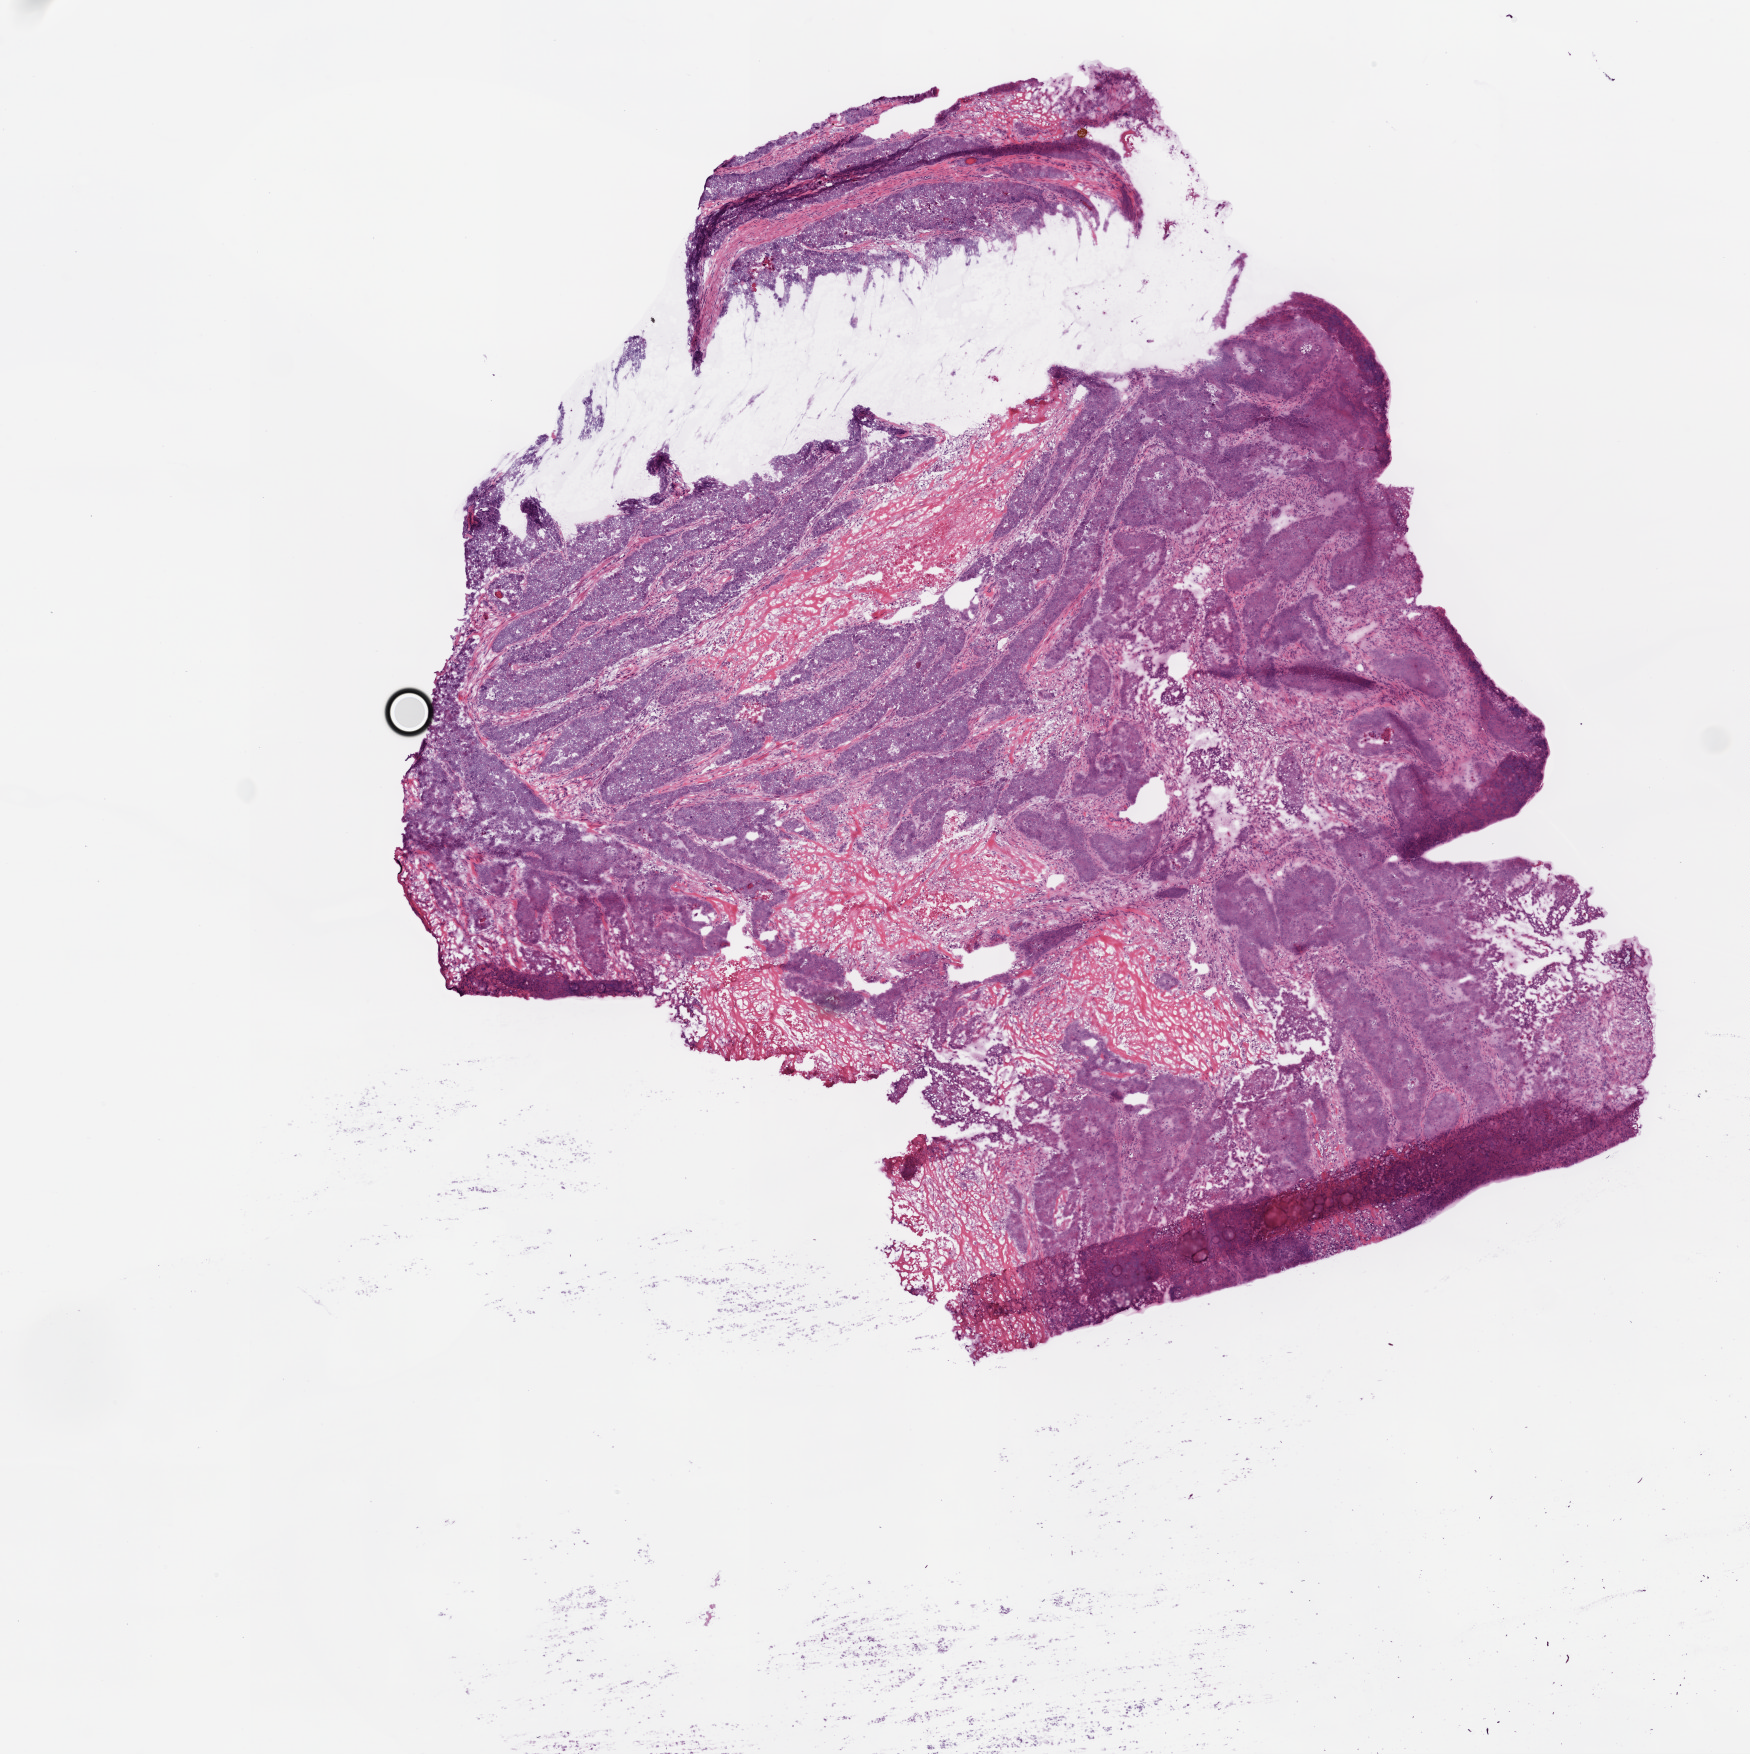
Digitized H&E-stained tissue section (whole slide), whole scanned area (about 7.0 x 7.0 mm, slide scanned at 20x) shown as a low-resolution overview. Frozen section from the top of the tissue portion. Sample: primary tumour, colon. Patient: male, age at initial diagnosis 68 years. Slide review estimates, as recorded: tumour cells 65%, tumour nuclei 90%, normal cells 0%, stromal cells 34%, necrosis 1%.
- lymph nodes positive (case pathology): 6 of 14 examined
- histologic diagnosis: Adenocarcinoma, NOS (descending colon)
- AJCC pathologic stage: IIIC